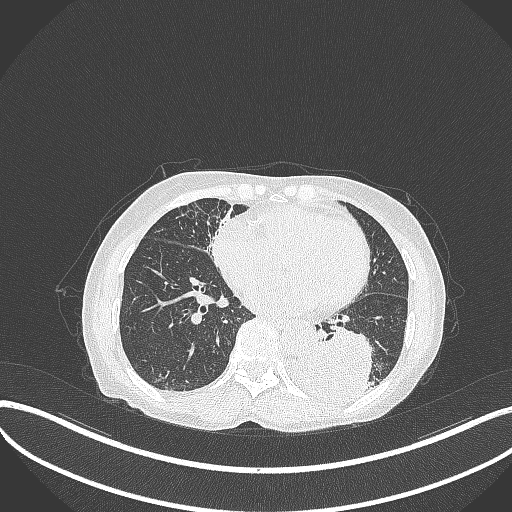
Chest CT, one axial slice; slice 112 of 370 in the series (ordered by position); reconstruction kernel B70f; 120 kVp; lung window (W 1500 / L -600 HU); 1 mm slice thickness; 512 × 512 image matrix, field of view 400 × 400 mm. Female patient, age 78 years. Case-level facts recorded for this patient, not image findings: clinical TNM (as recorded): T3 N0 M1.
Structures marked on this image (rectangle marked by the reading radiologist):
- lung tumour (recorded histology: squamous cell carcinoma): bounding box [x1, y1, x2, y2] px = [289, 327, 378, 410]